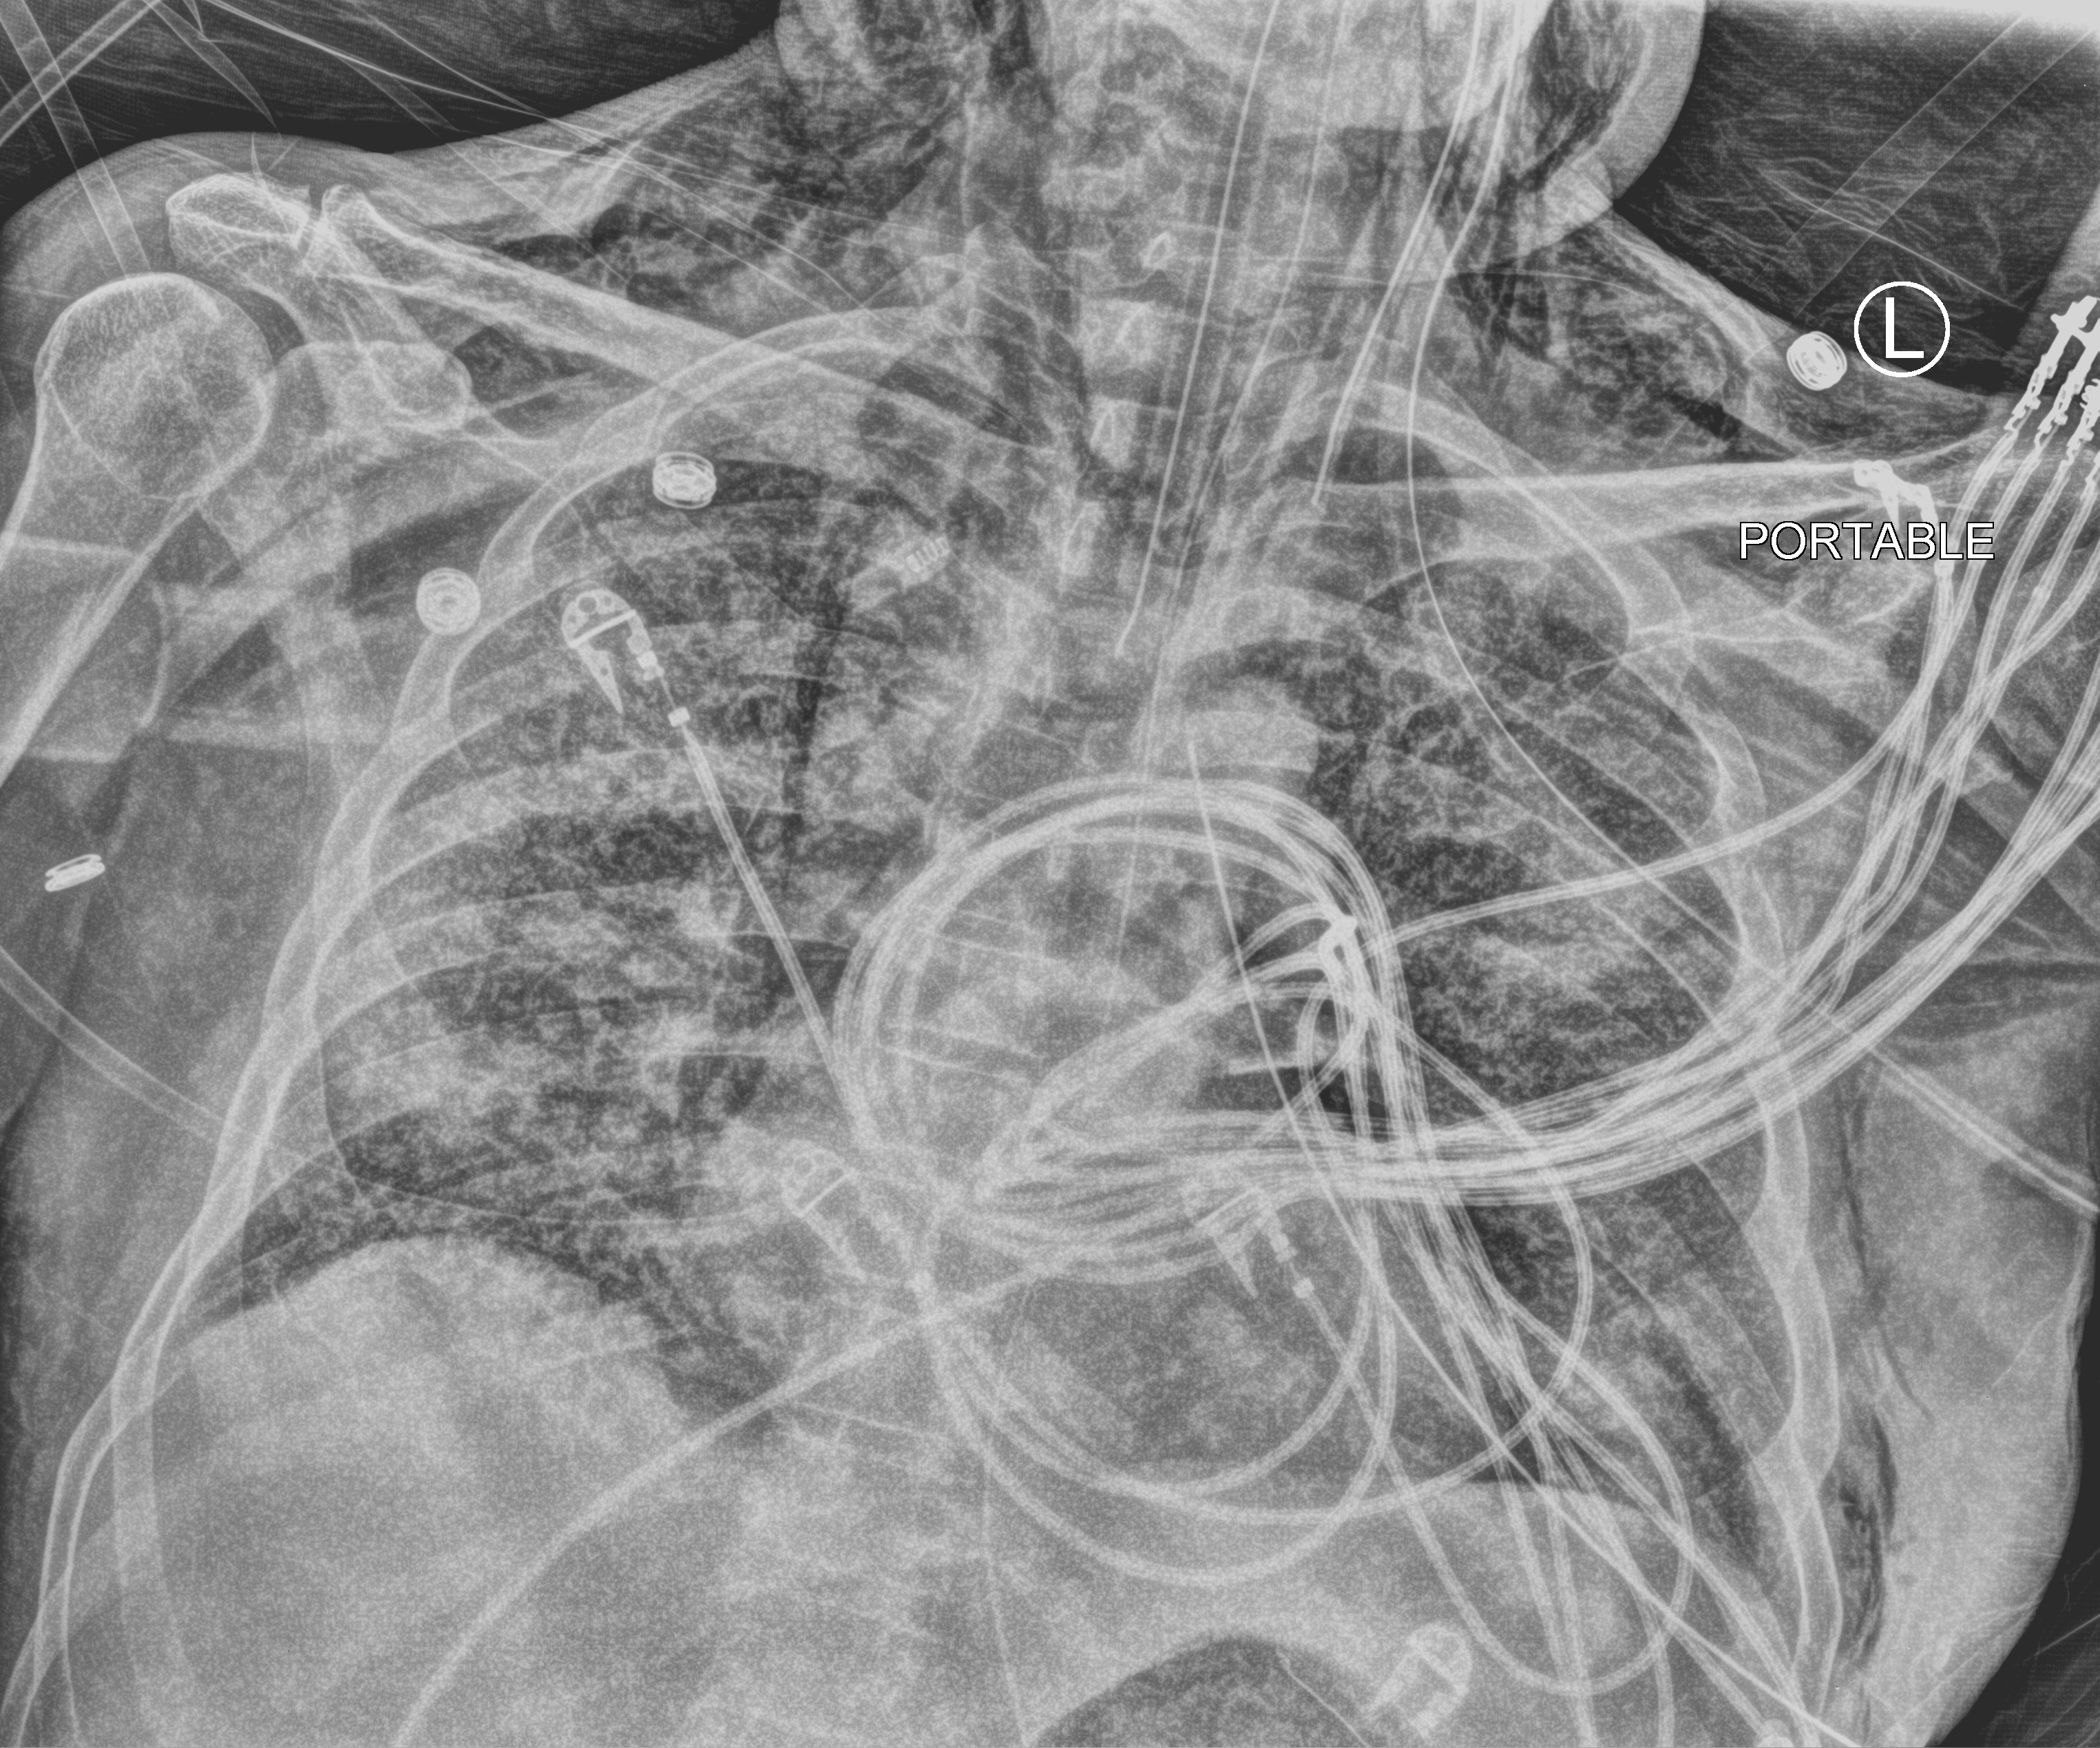
Portable chest radiograph. Male patient hospitalised with COVID-19, age 60–74 years.
Hospital-stay facts (about this admission, not read from this image; timing relative to this image not recorded): admitted to intensive care during this hospital stay: yes; mechanically ventilated during this hospital stay: yes.